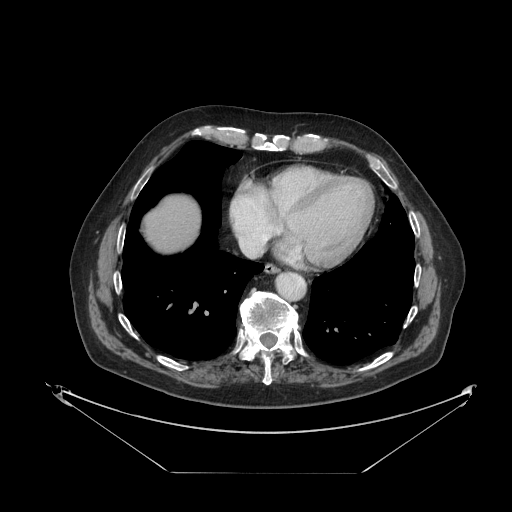
Contrast-enhanced abdominal CT, one axial slice; position 120 of 121 along the scan axis; 120 kVp; intravenous contrast given; soft-tissue window (W 400 / L 40 HU); 2.5 mm slice thickness; 512 × 512 image matrix, field of view 500 × 500 mm. Male patient, age 68 years. From the clinical record (not read from this slice): diagnosis: colorectal cancer liver metastases, imaged before liver resection; multiple liver metastases: no; largest metastasis: 4 cm; chemotherapy before resection: yes.
Structures marked on this image (expert manual segmentation):
- liver: bounding box (x1, y1, x2, y2) in pixels: (144, 196, 200, 251)
- planned liver remnant (the part of the liver to remain after resection): (144, 196, 200, 251)